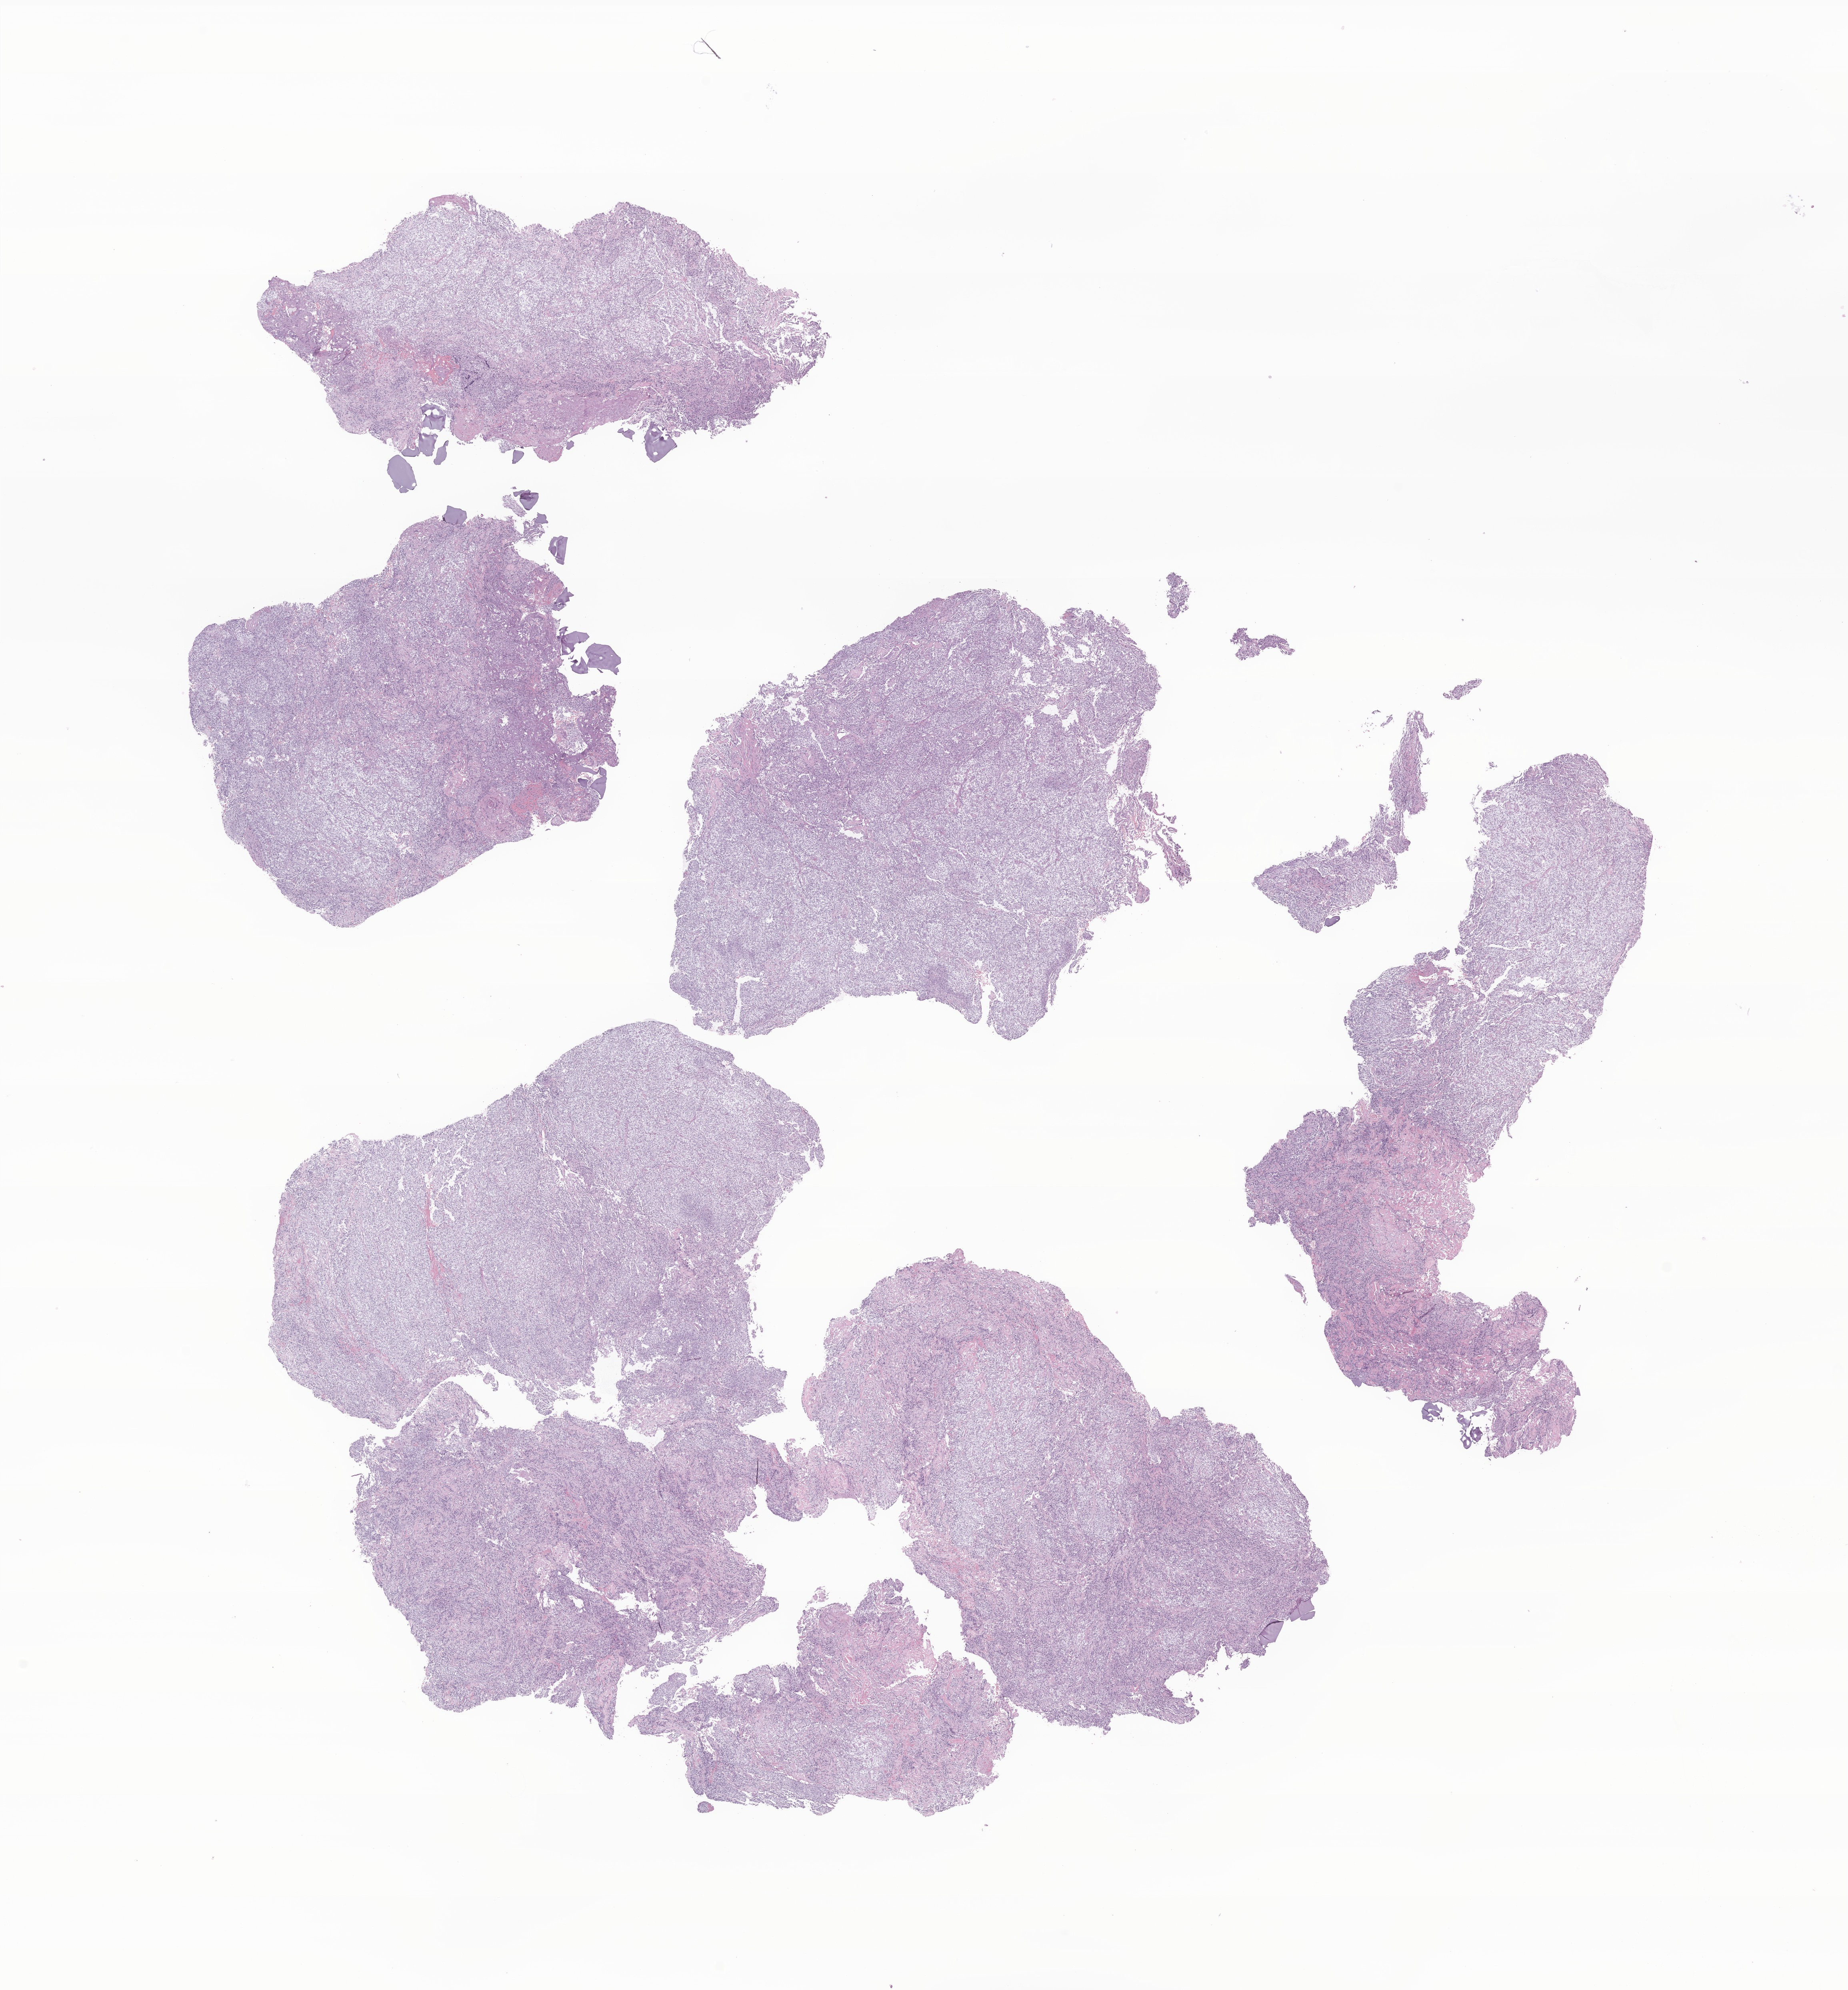
Digitized hematoxylin and eosin (H&E)-stained section of tumor tissue from the brain — whole scanned area (about 19.5 x 21.0 mm) shown as a low-resolution overview; formalin-fixed paraffin-embedded section. Female patient, age 147 months.
• diagnosis: Neoplasm, uncertain whether benign or malignant